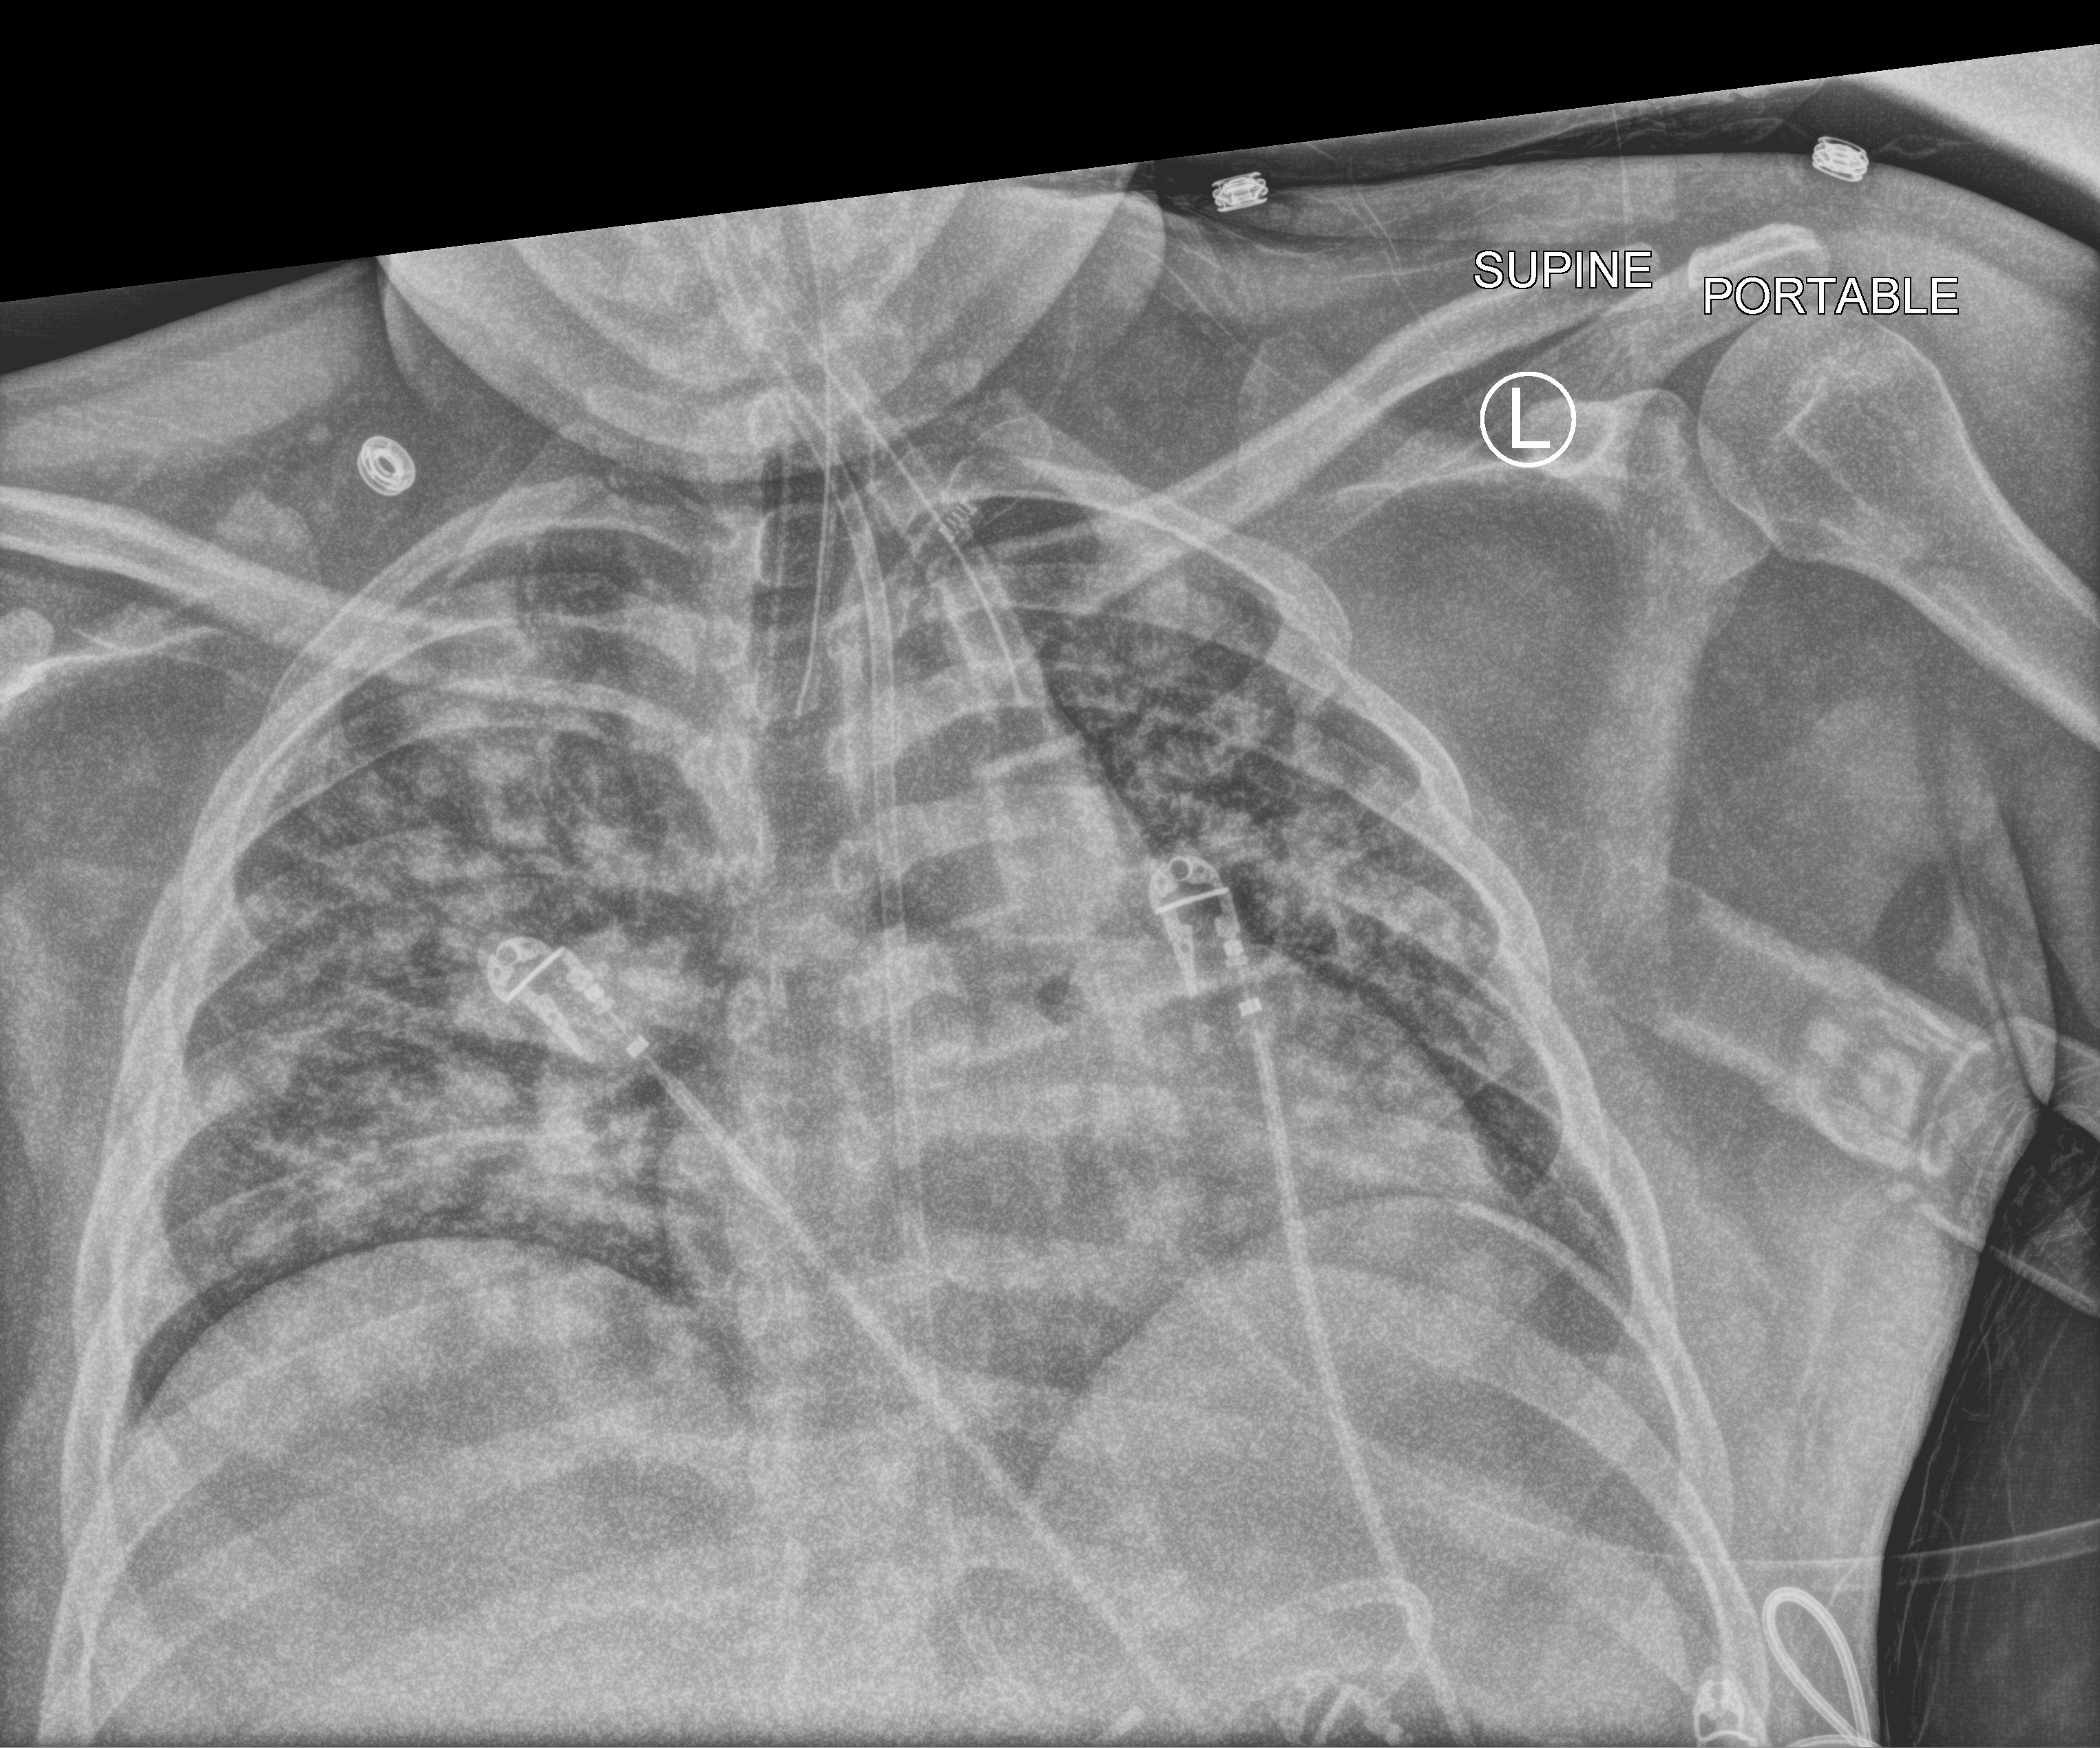
Chest X-ray (portable); anteroposterior (AP) projection. Male patient hospitalised with COVID-19, age 18–59 years.
Hospital-stay facts (about this admission, not read from this image; timing relative to this image not recorded):
- chronic kidney disease (admission record): no
- COPD (admission record): no
- mechanically ventilated during this hospital stay: yes